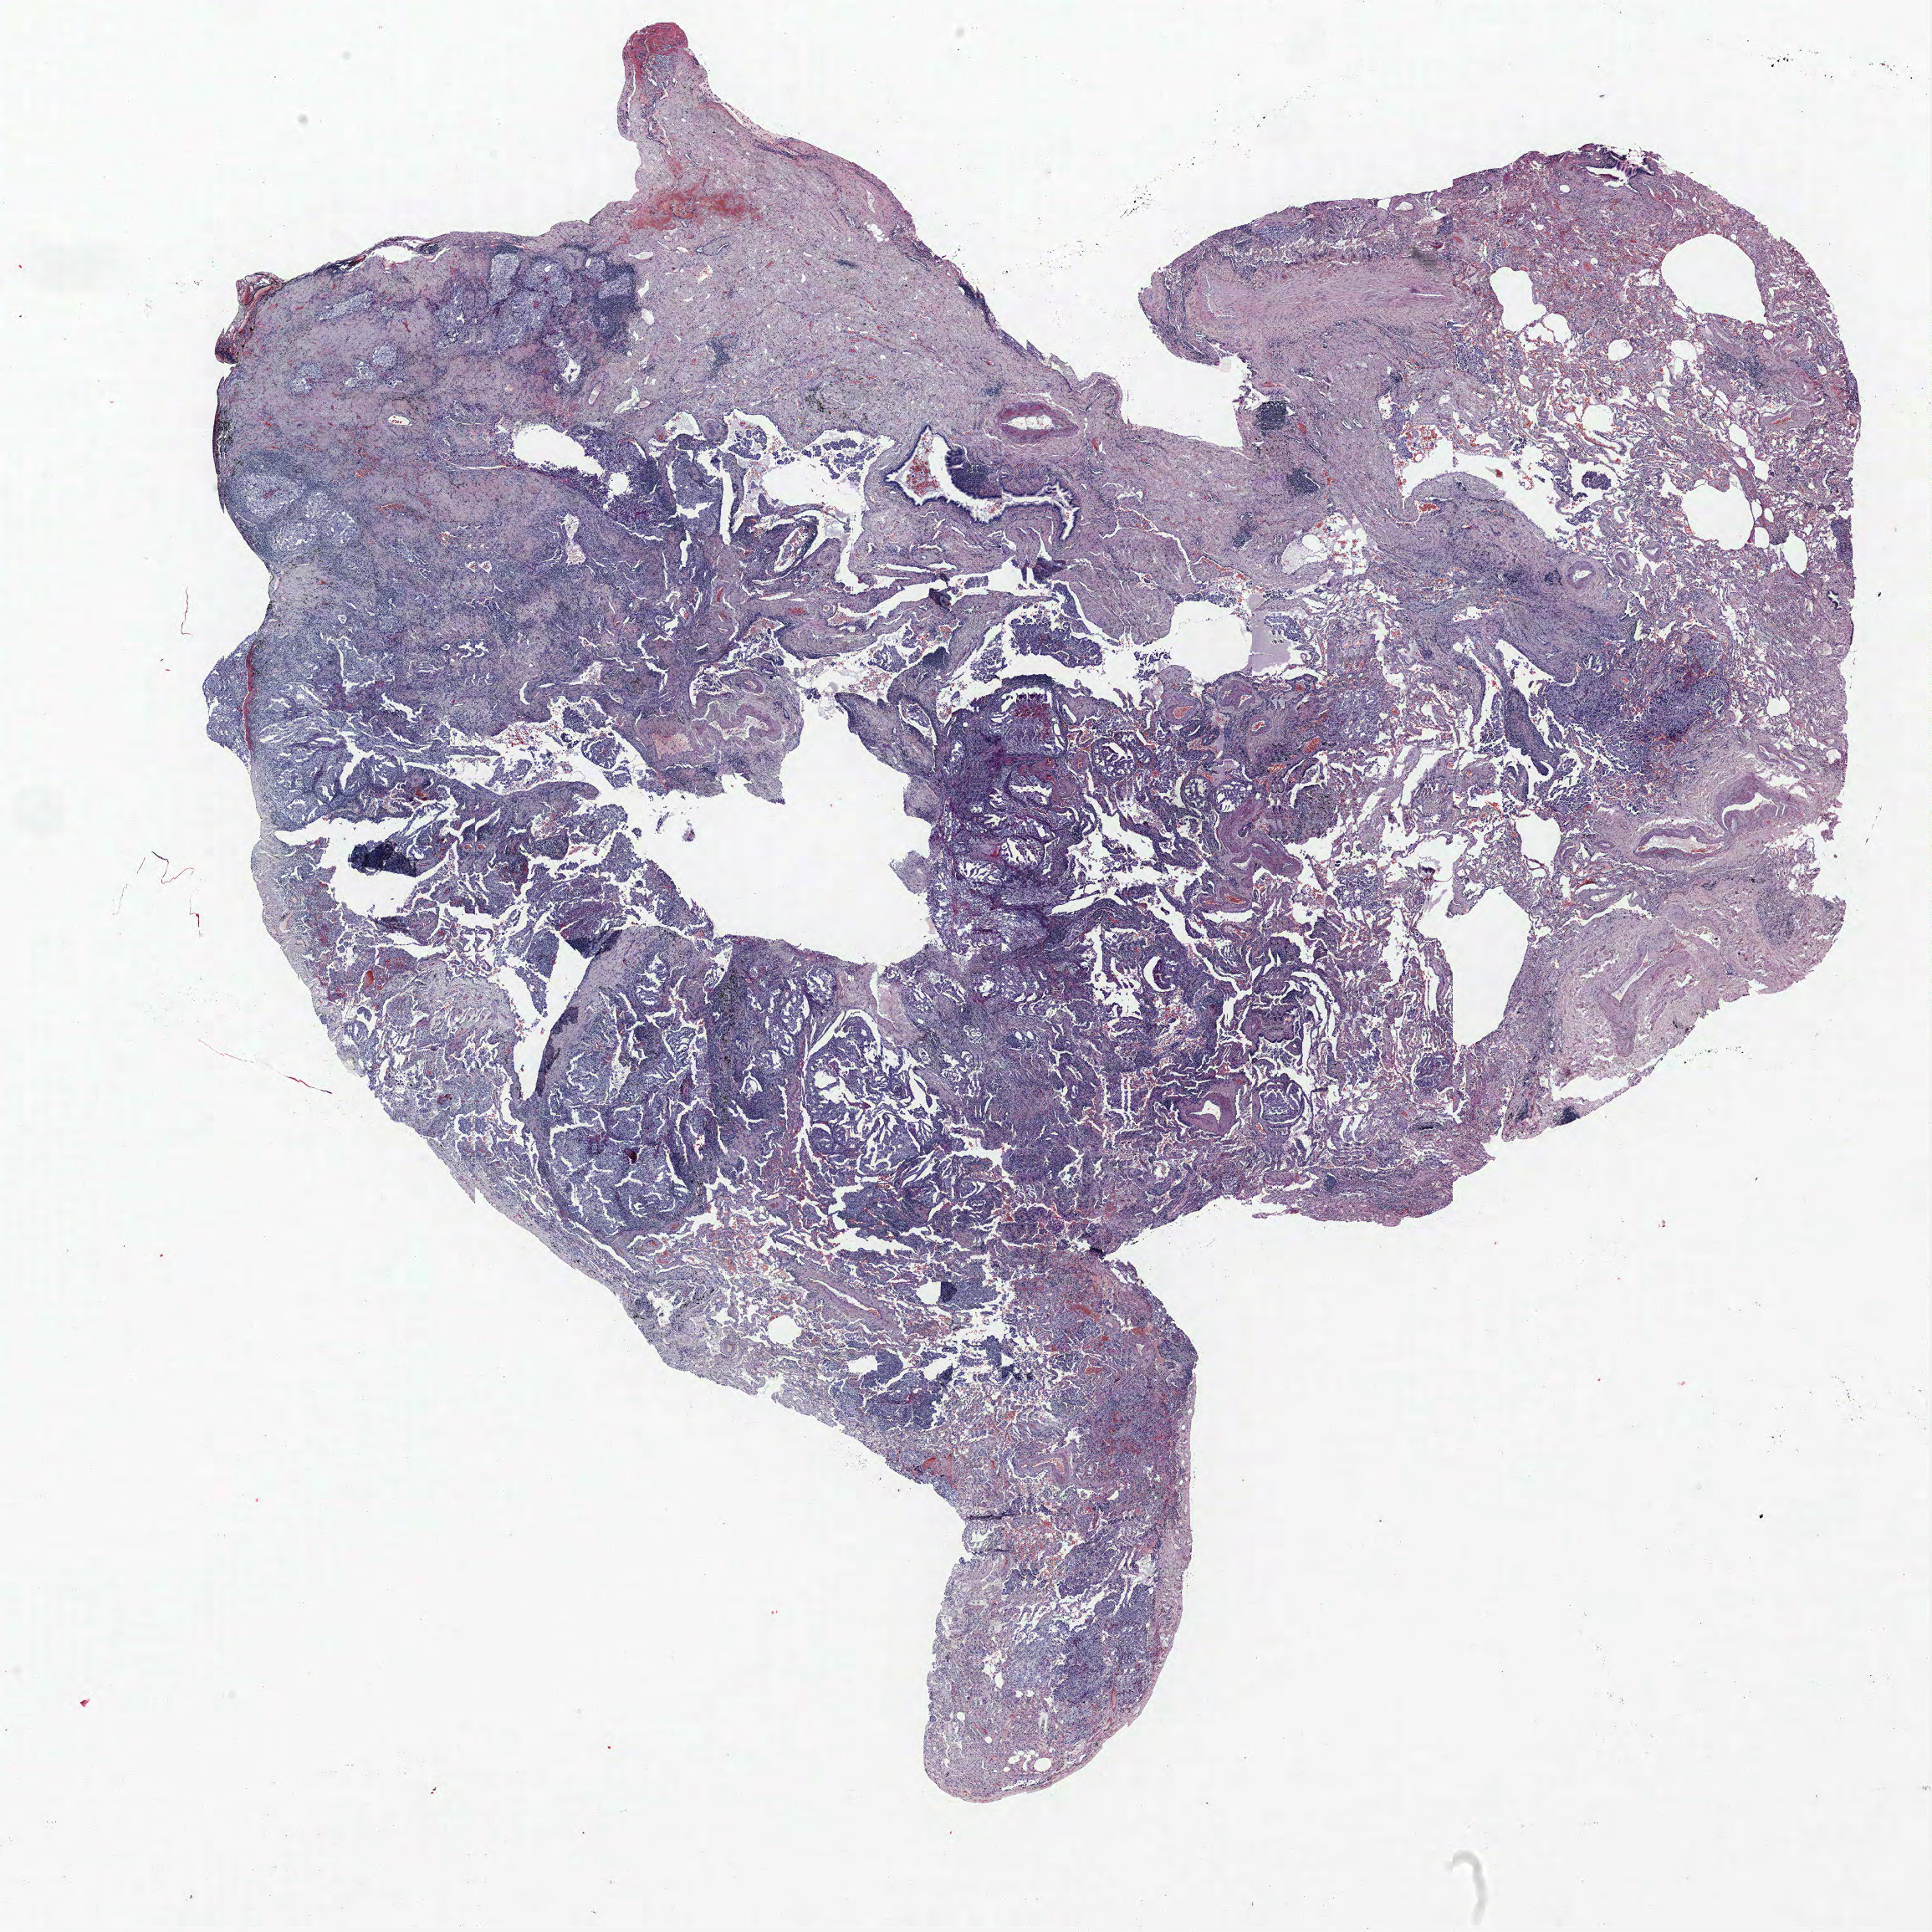
H&E-stained whole-slide image, shown as a low-resolution overview of the whole scanned area (about 18.5 x 18.5 mm, slide scanned at 40x). FFPE section. Lung tissue. Male, age 67 at enrolment.
Participant's lung-cancer diagnosis: Squamous cell carcinoma, NOS (ICD-O-3 8070/3).